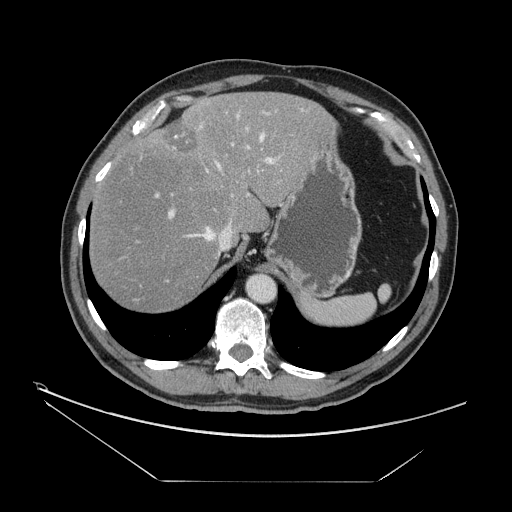
Contrast-enhanced abdominal CT, one axial slice. Position 118 of 161 along the scan axis. Reconstruction kernel STANDARD. 120 kVp. Intravenous contrast given. Soft-tissue window (W 400 / L 40 HU). 2.5 mm slice thickness. 512 × 512 image matrix, field of view 440 × 440 mm. Male patient, age 65 years. Case-level facts recorded for this patient, not image findings: diagnosis: colorectal cancer liver metastases, imaged before liver resection.
Structures marked on this image (expert manual segmentation):
- hepatic veins: bounding box (x1, y1, x2, y2) in pixels: (185, 134, 264, 255)
- liver: (90, 92, 332, 313)
- planned liver remnant (the part of the liver to remain after resection): (90, 93, 331, 313)
- portal vein (with intrahepatic branches): (155, 108, 306, 219)
- liver metastasis: (161, 119, 196, 154)